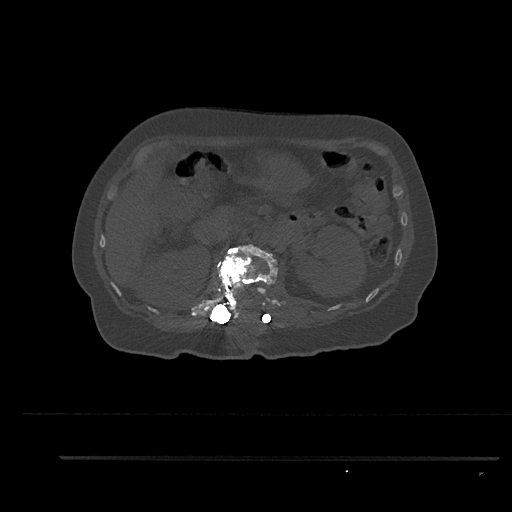
CT including the spine, one axial slice; slice 209 of 797 in the series (ordered by position); 120 kVp; bone window (W 1800 / L 400 HU); 0.5 mm slice thickness; 512 × 512 image matrix, field of view 408 × 408 mm. Patient: female, 44 years. From the clinical record (not read from this slice): primary cancer: renal.
Structures marked on this image (semi-automatically segmented with operator editing):
- L1 vertebra: bounding box (x1, y1, x2, y2) in pixels: (203, 244, 278, 322)